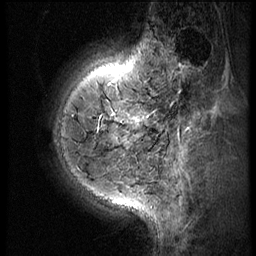
Breast MRI (dynamic contrast-enhanced), one sagittal slice. Slice 15 of 60 in the series (ordered by position). 3 images stored at this slice position (order not interpretable as contrast timing). 1.5 T. TE 4.2 ms, TR 9 ms. 2.5 mm slice thickness. 256 × 256 image matrix, field of view 180 × 180 mm. Patient: female, 38 years. Case-level facts recorded for this patient, not image findings: setting: breast cancer imaged before/during neoadjuvant chemotherapy; receptor status: triple-negative.
Structures marked on this image (semi-automatic segmentation, software-assisted and operator-edited):
- analysis volume of interest (the breast-tissue region the enhancement analysis was run in; not a lesion): bounding box [x1, y1, x2, y2] px = [119, 93, 165, 150]
- tumour enhancement mask (voxels above the 140 % enhancement threshold inside the analysis volume of interest): [127, 119, 145, 125]